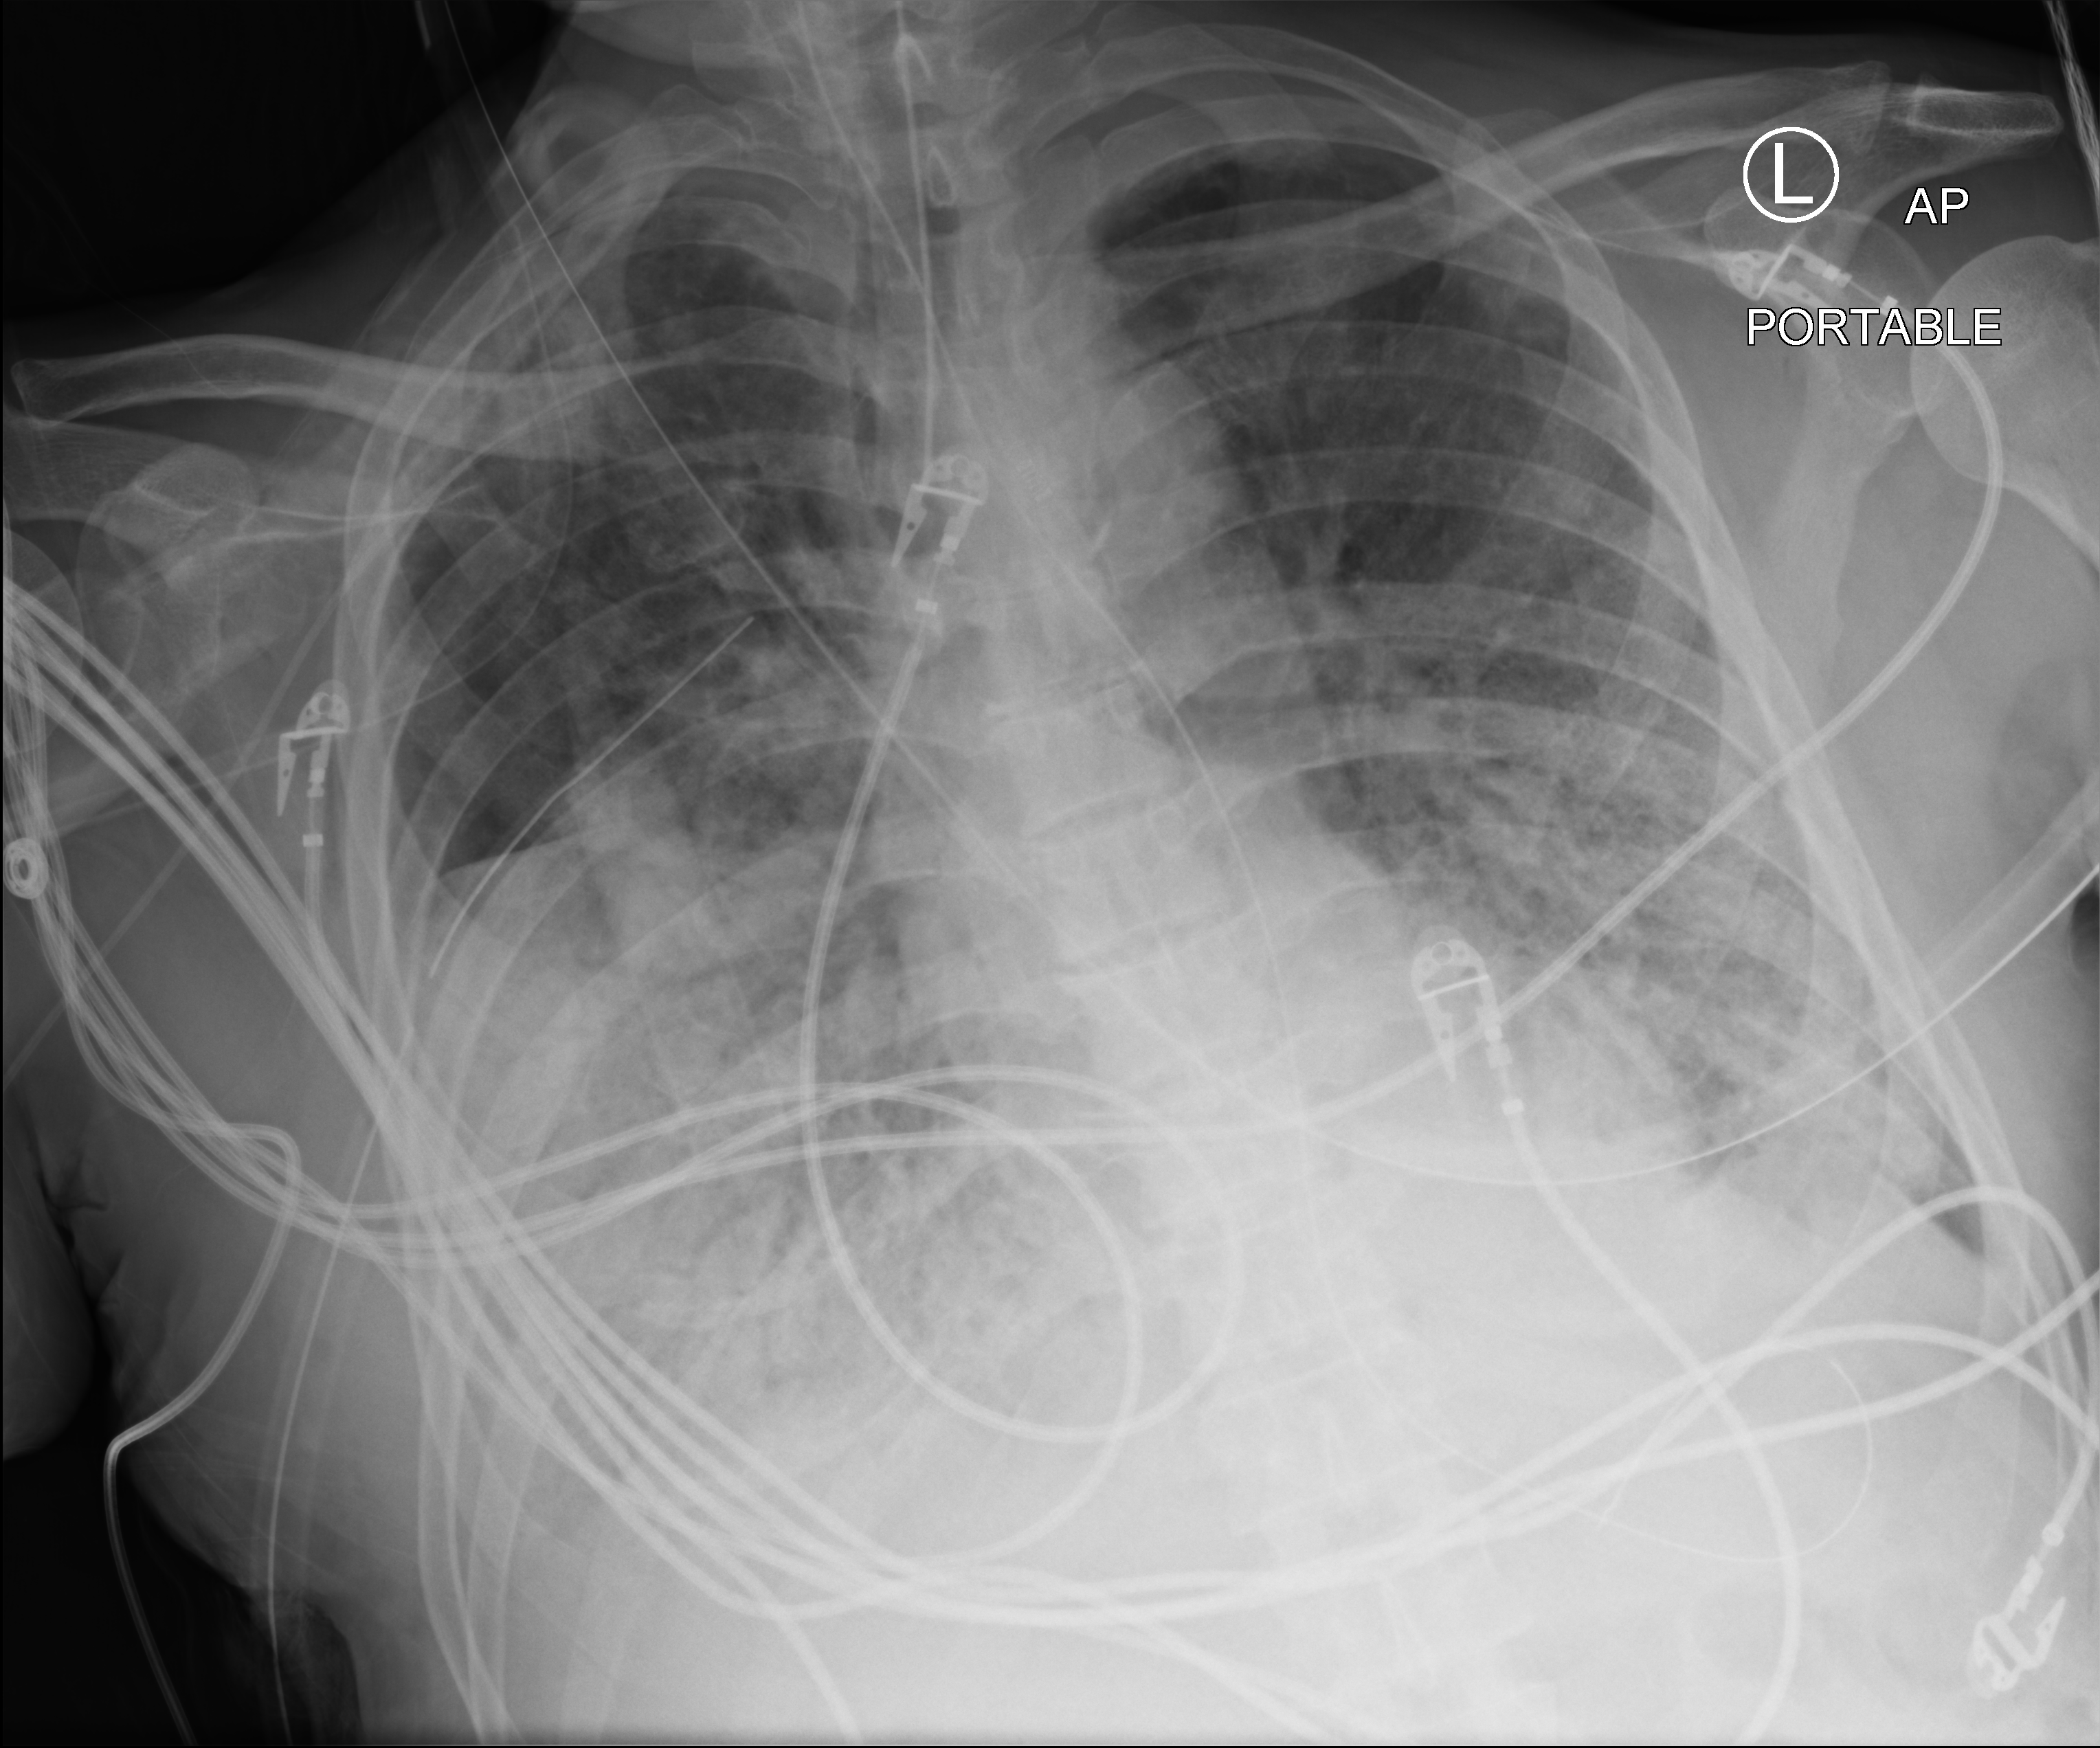
Bedside chest radiograph (computed radiography); anteroposterior (AP) projection. Male patient hospitalised with COVID-19, age 60–74 years.
Hospital-stay facts (about this admission, not read from this image; timing relative to this image not recorded):
- other chronic lung disease (admission record): no